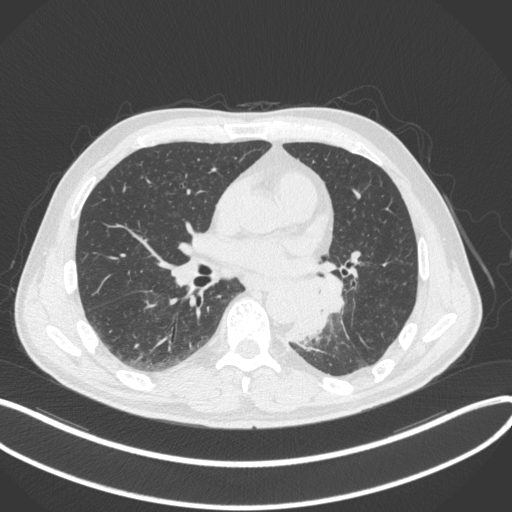
Chest CT, one axial slice; position 163 of 328 along the scan axis; reconstruction kernel B31f; 120 kVp; lung window (W 1500 / L -600 HU); 1 mm slice thickness; 512 × 512 image matrix. Male patient, age 59 years. Case-level facts recorded for this patient, not image findings: clinical TNM (as recorded): T2a N2 M0.
Structures marked on this image (rectangle marked by the reading radiologist):
- lung tumour (recorded histology: squamous cell carcinoma): bounding box [x1, y1, x2, y2] px = [276, 271, 344, 348]